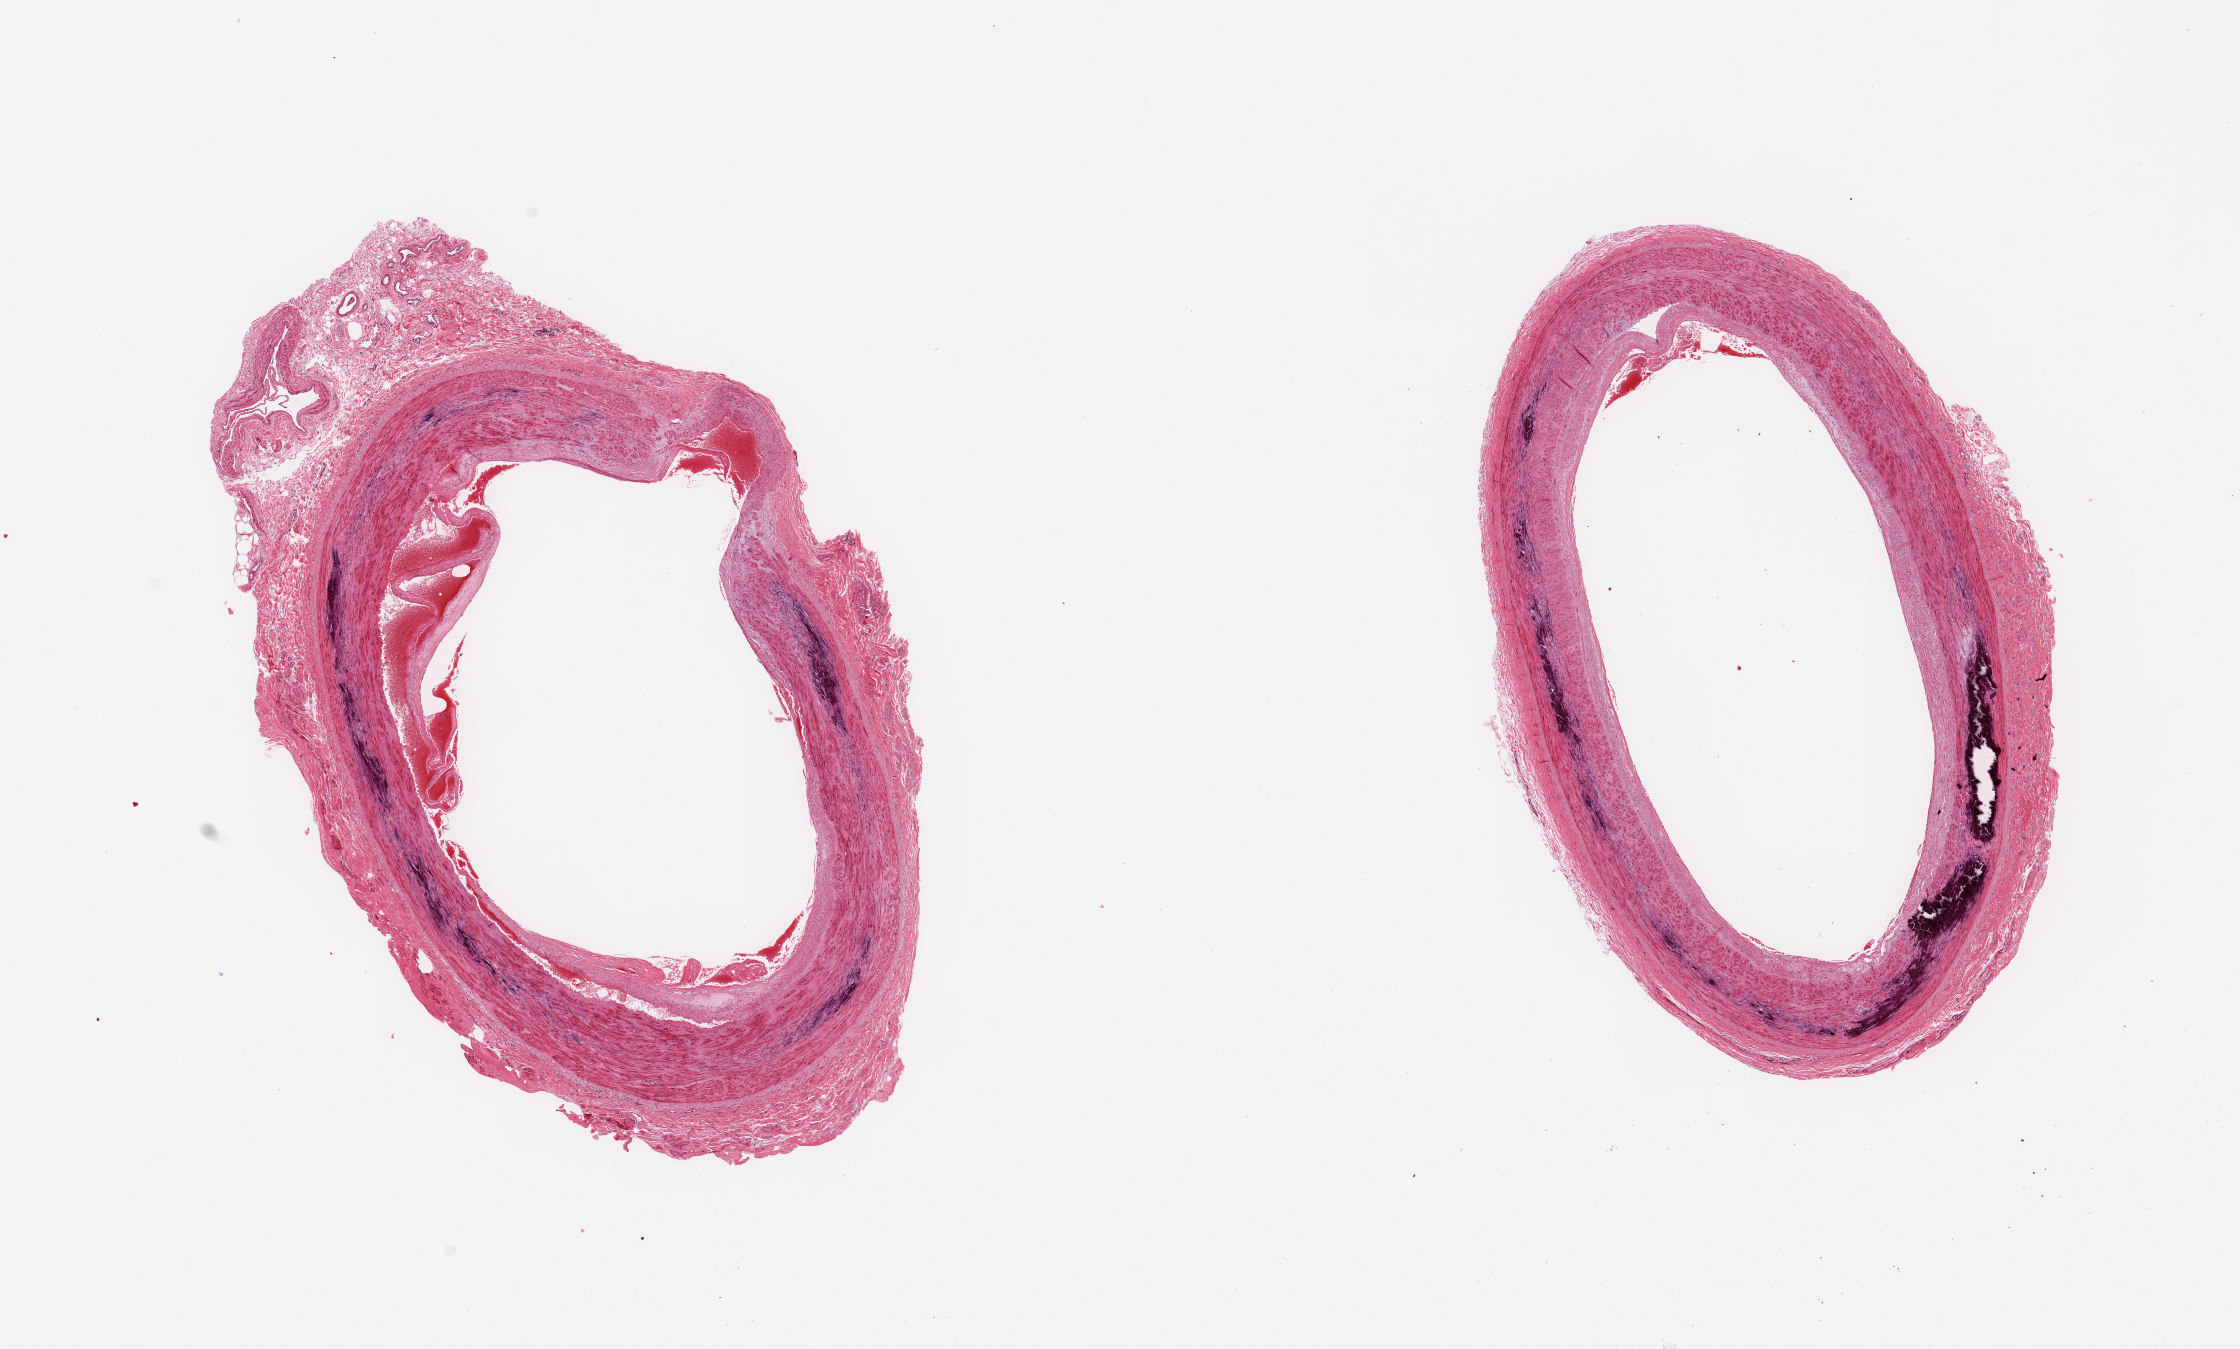
Haematoxylin and eosin whole-slide image, shown as a low-resolution overview of the whole scanned area (about 17.7 x 10.7 mm). PAXgene-fixed paraffin-embedded (PFPE) section. Target tissue: tibial artery. Donor tissue sample. Donor sex: female.
* reviewer comment on this tissue sample: 2 pieces; widely patent; moderate medial calcification